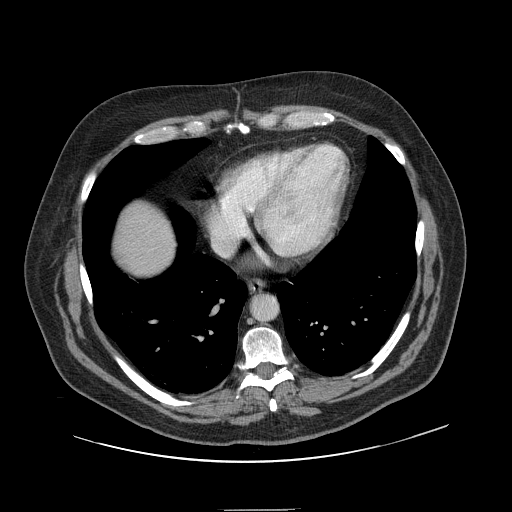
Contrast-enhanced abdominal CT, one axial slice; position 143 of 154 along the scan axis; 120 kVp; soft-tissue window (W 400 / L 40 HU); 2.5 mm slice thickness; 512 × 512 image matrix, field of view 451 × 451 mm. Male patient, age 61 years. Case-level facts recorded for this patient, not image findings: diagnosis: colorectal cancer liver metastases, imaged before liver resection; multiple liver metastases: yes; largest metastasis: 2.6 cm; disease in both lobes: yes.
Structures marked on this image (expert manual segmentation):
- liver: bounding box <116,203,174,275> (left, top, right, bottom; pixels)
- planned liver remnant (the part of the liver to remain after resection): <116,203,174,276>